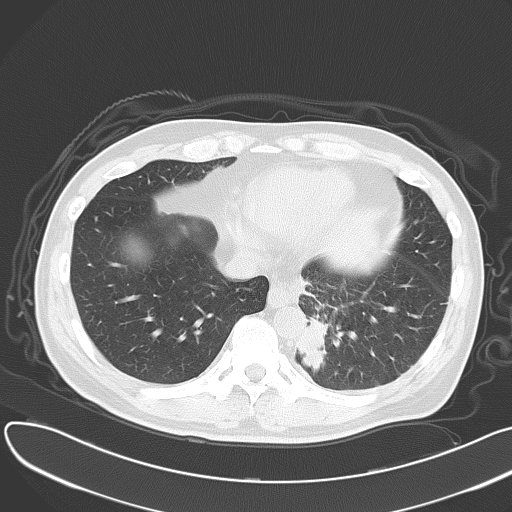
Chest CT, one axial slice. Slice 14 of 55 in the series (ordered by position). Reconstruction kernel B70f. Lung window (W 1500 / L -600 HU). 5 mm slice thickness. 512 × 512 image matrix. Patient: male, 55 years. Case-level facts recorded for this patient, not image findings: clinical TNM (as recorded): T2 N3 M0.
Annotated regions visible in this slice (bounding box drawn by a radiologist):
- lung tumour (recorded histology: small cell carcinoma): bounding box <298,314,333,377> (left, top, right, bottom; pixels)